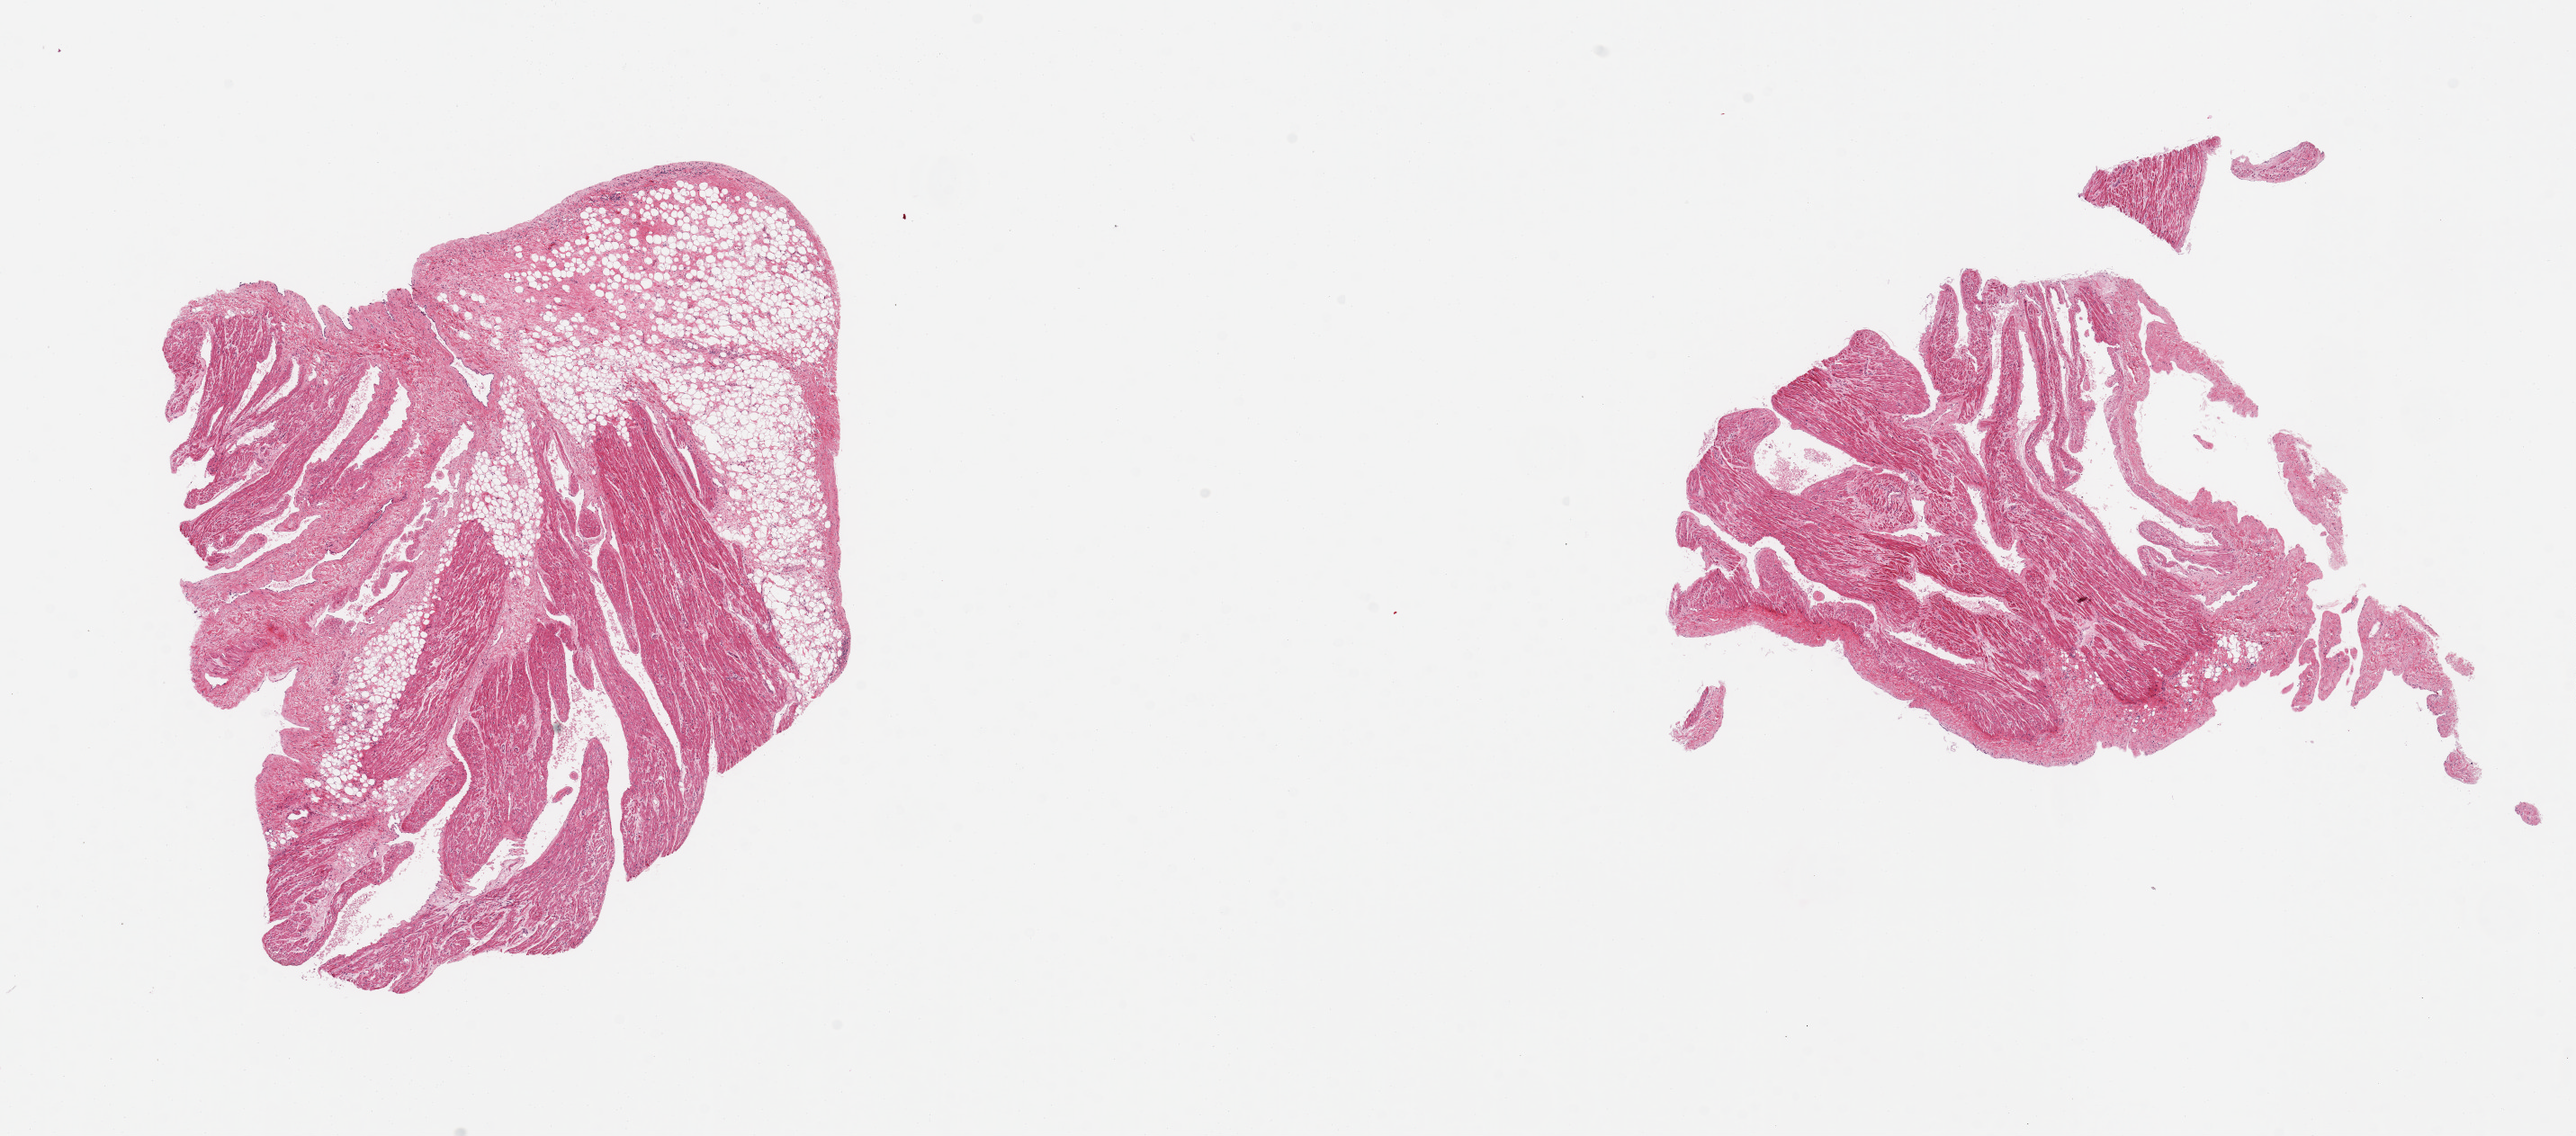
Whole-slide image, hematoxylin and eosin (H&E) stain, brightfield, low-resolution overview of the scanned area, about 22.6 x 10.0 mm, PAXgene-fixed, paraffin-embedded tissue, target tissue: auricular appendage, donor tissue sample. Female donor.
* review note (as recorded): 2 pieces; 1 piece has 50% fat content, internal and external